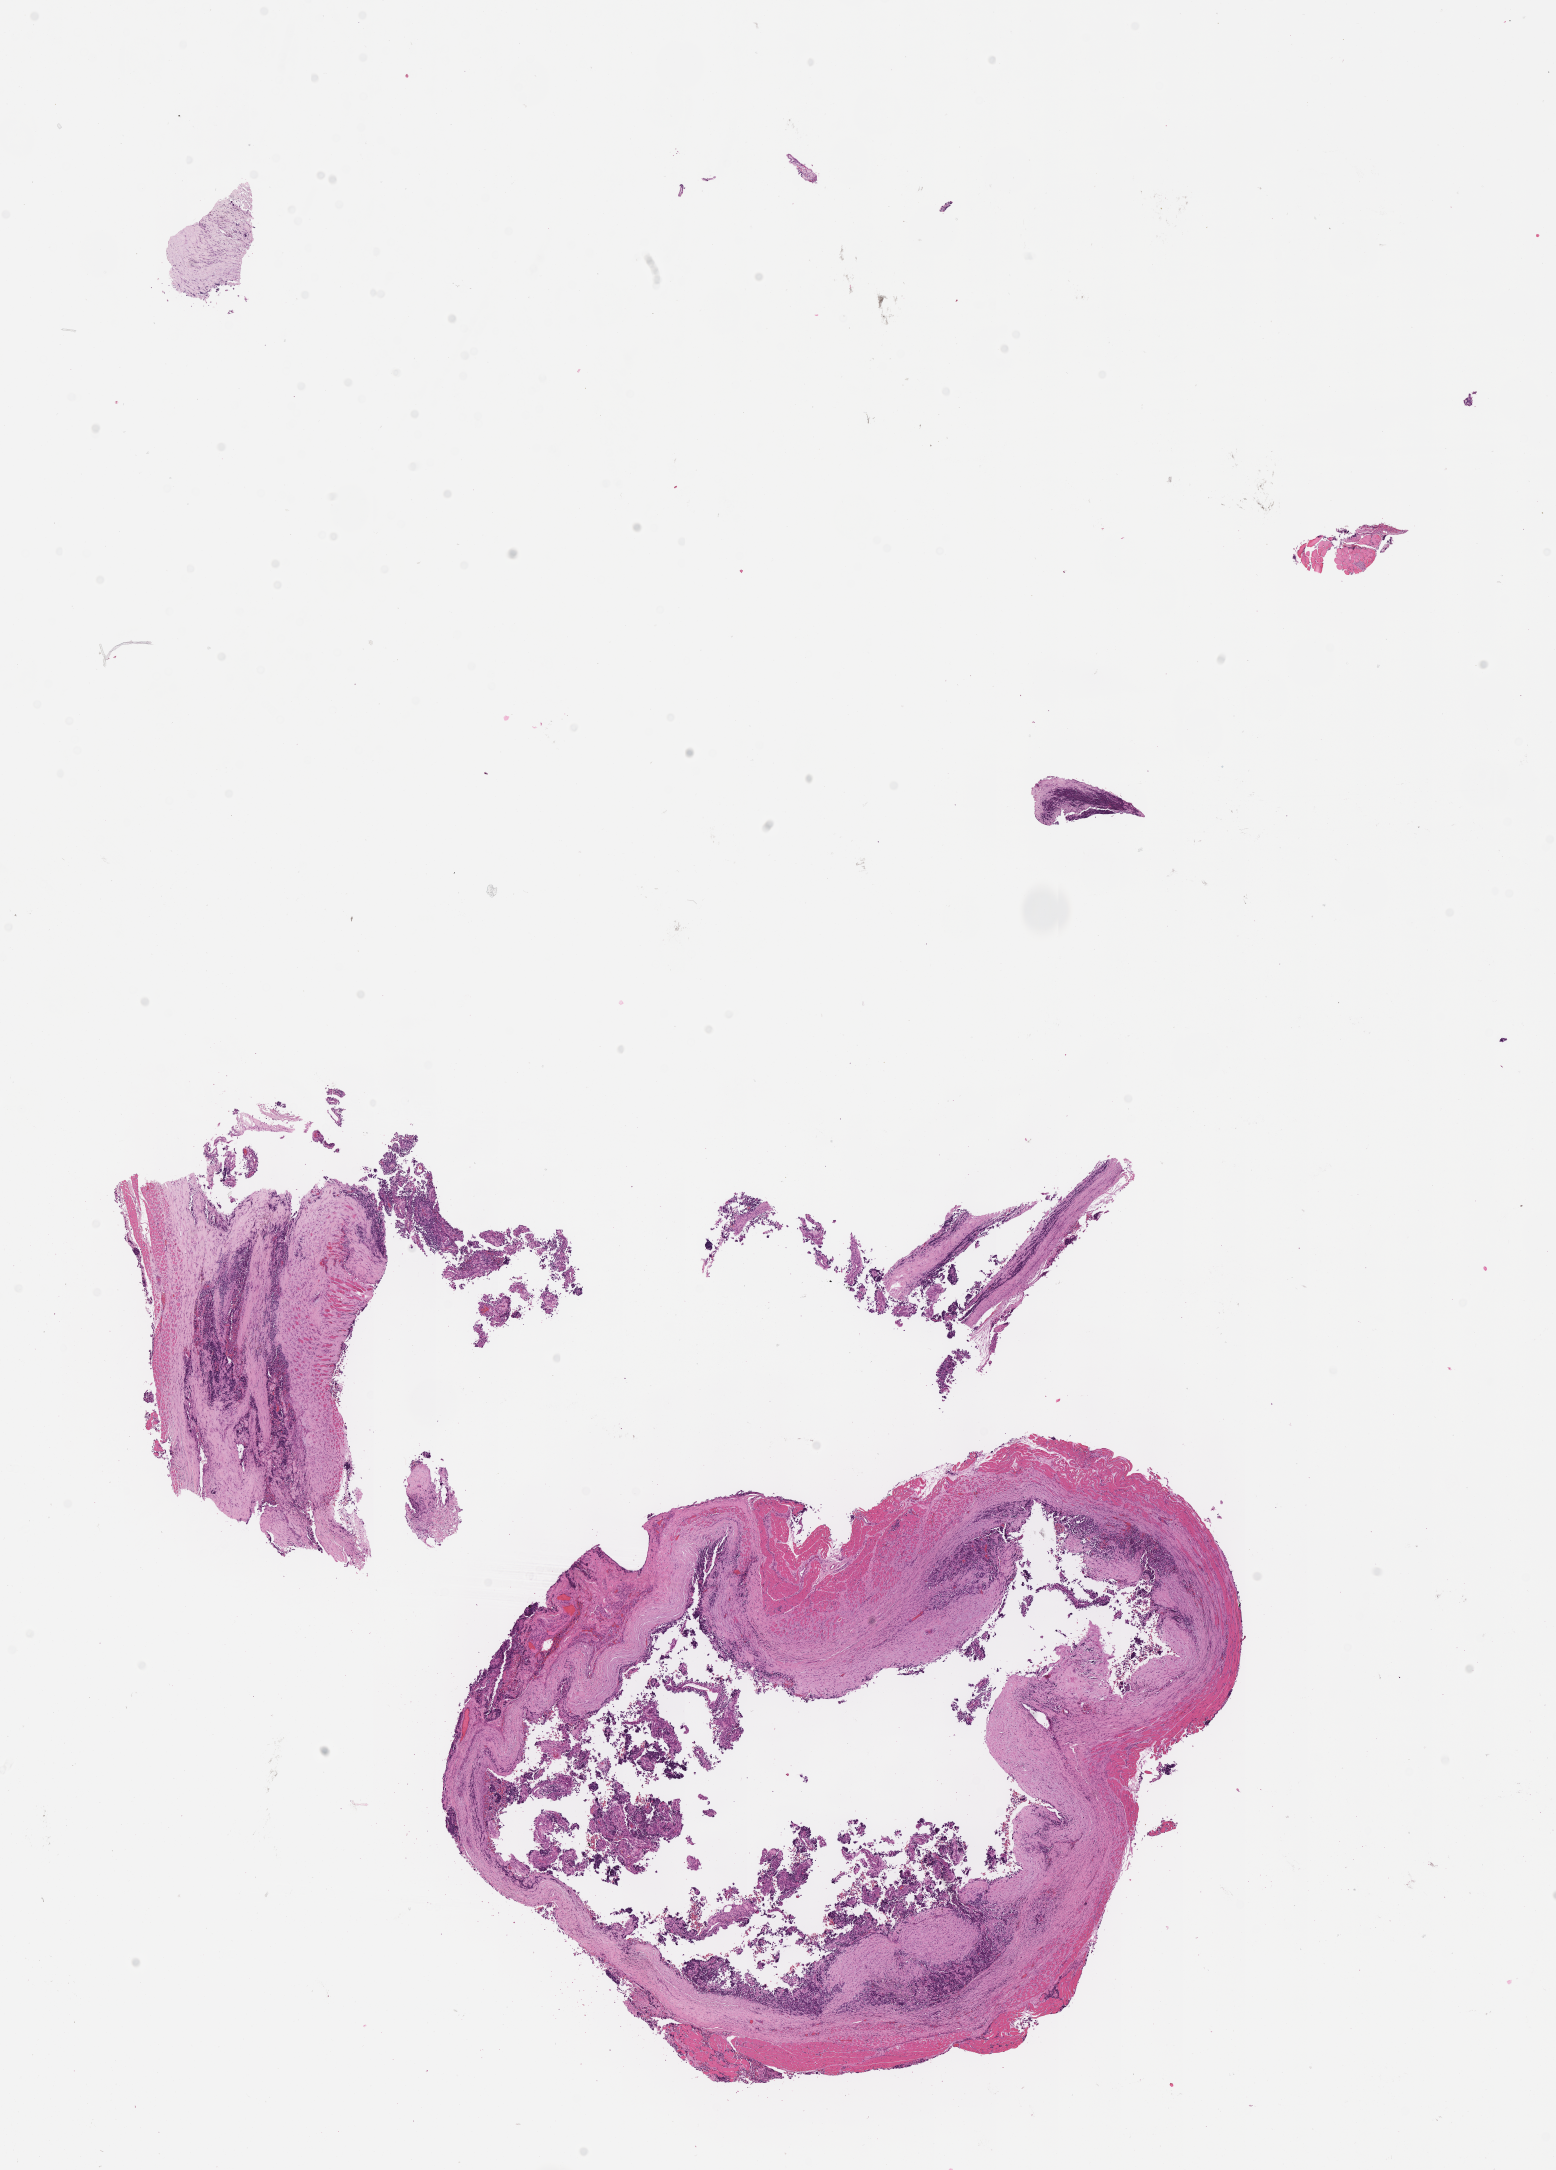
Whole-slide image, H&E stain of tumor tissue, low-resolution overview of the scanned area, about 12.6 x 17.5 mm. FFPE section. Site: abdominal wall, right. Patient: female, age 3.0 years at diagnosis.
• metastatic status at presentation (as recorded): non-metastatic
• diagnosis: rhabdomyosarcoma; histological classification: alveolar rhabdomyosarcoma
• stage (as recorded): 2